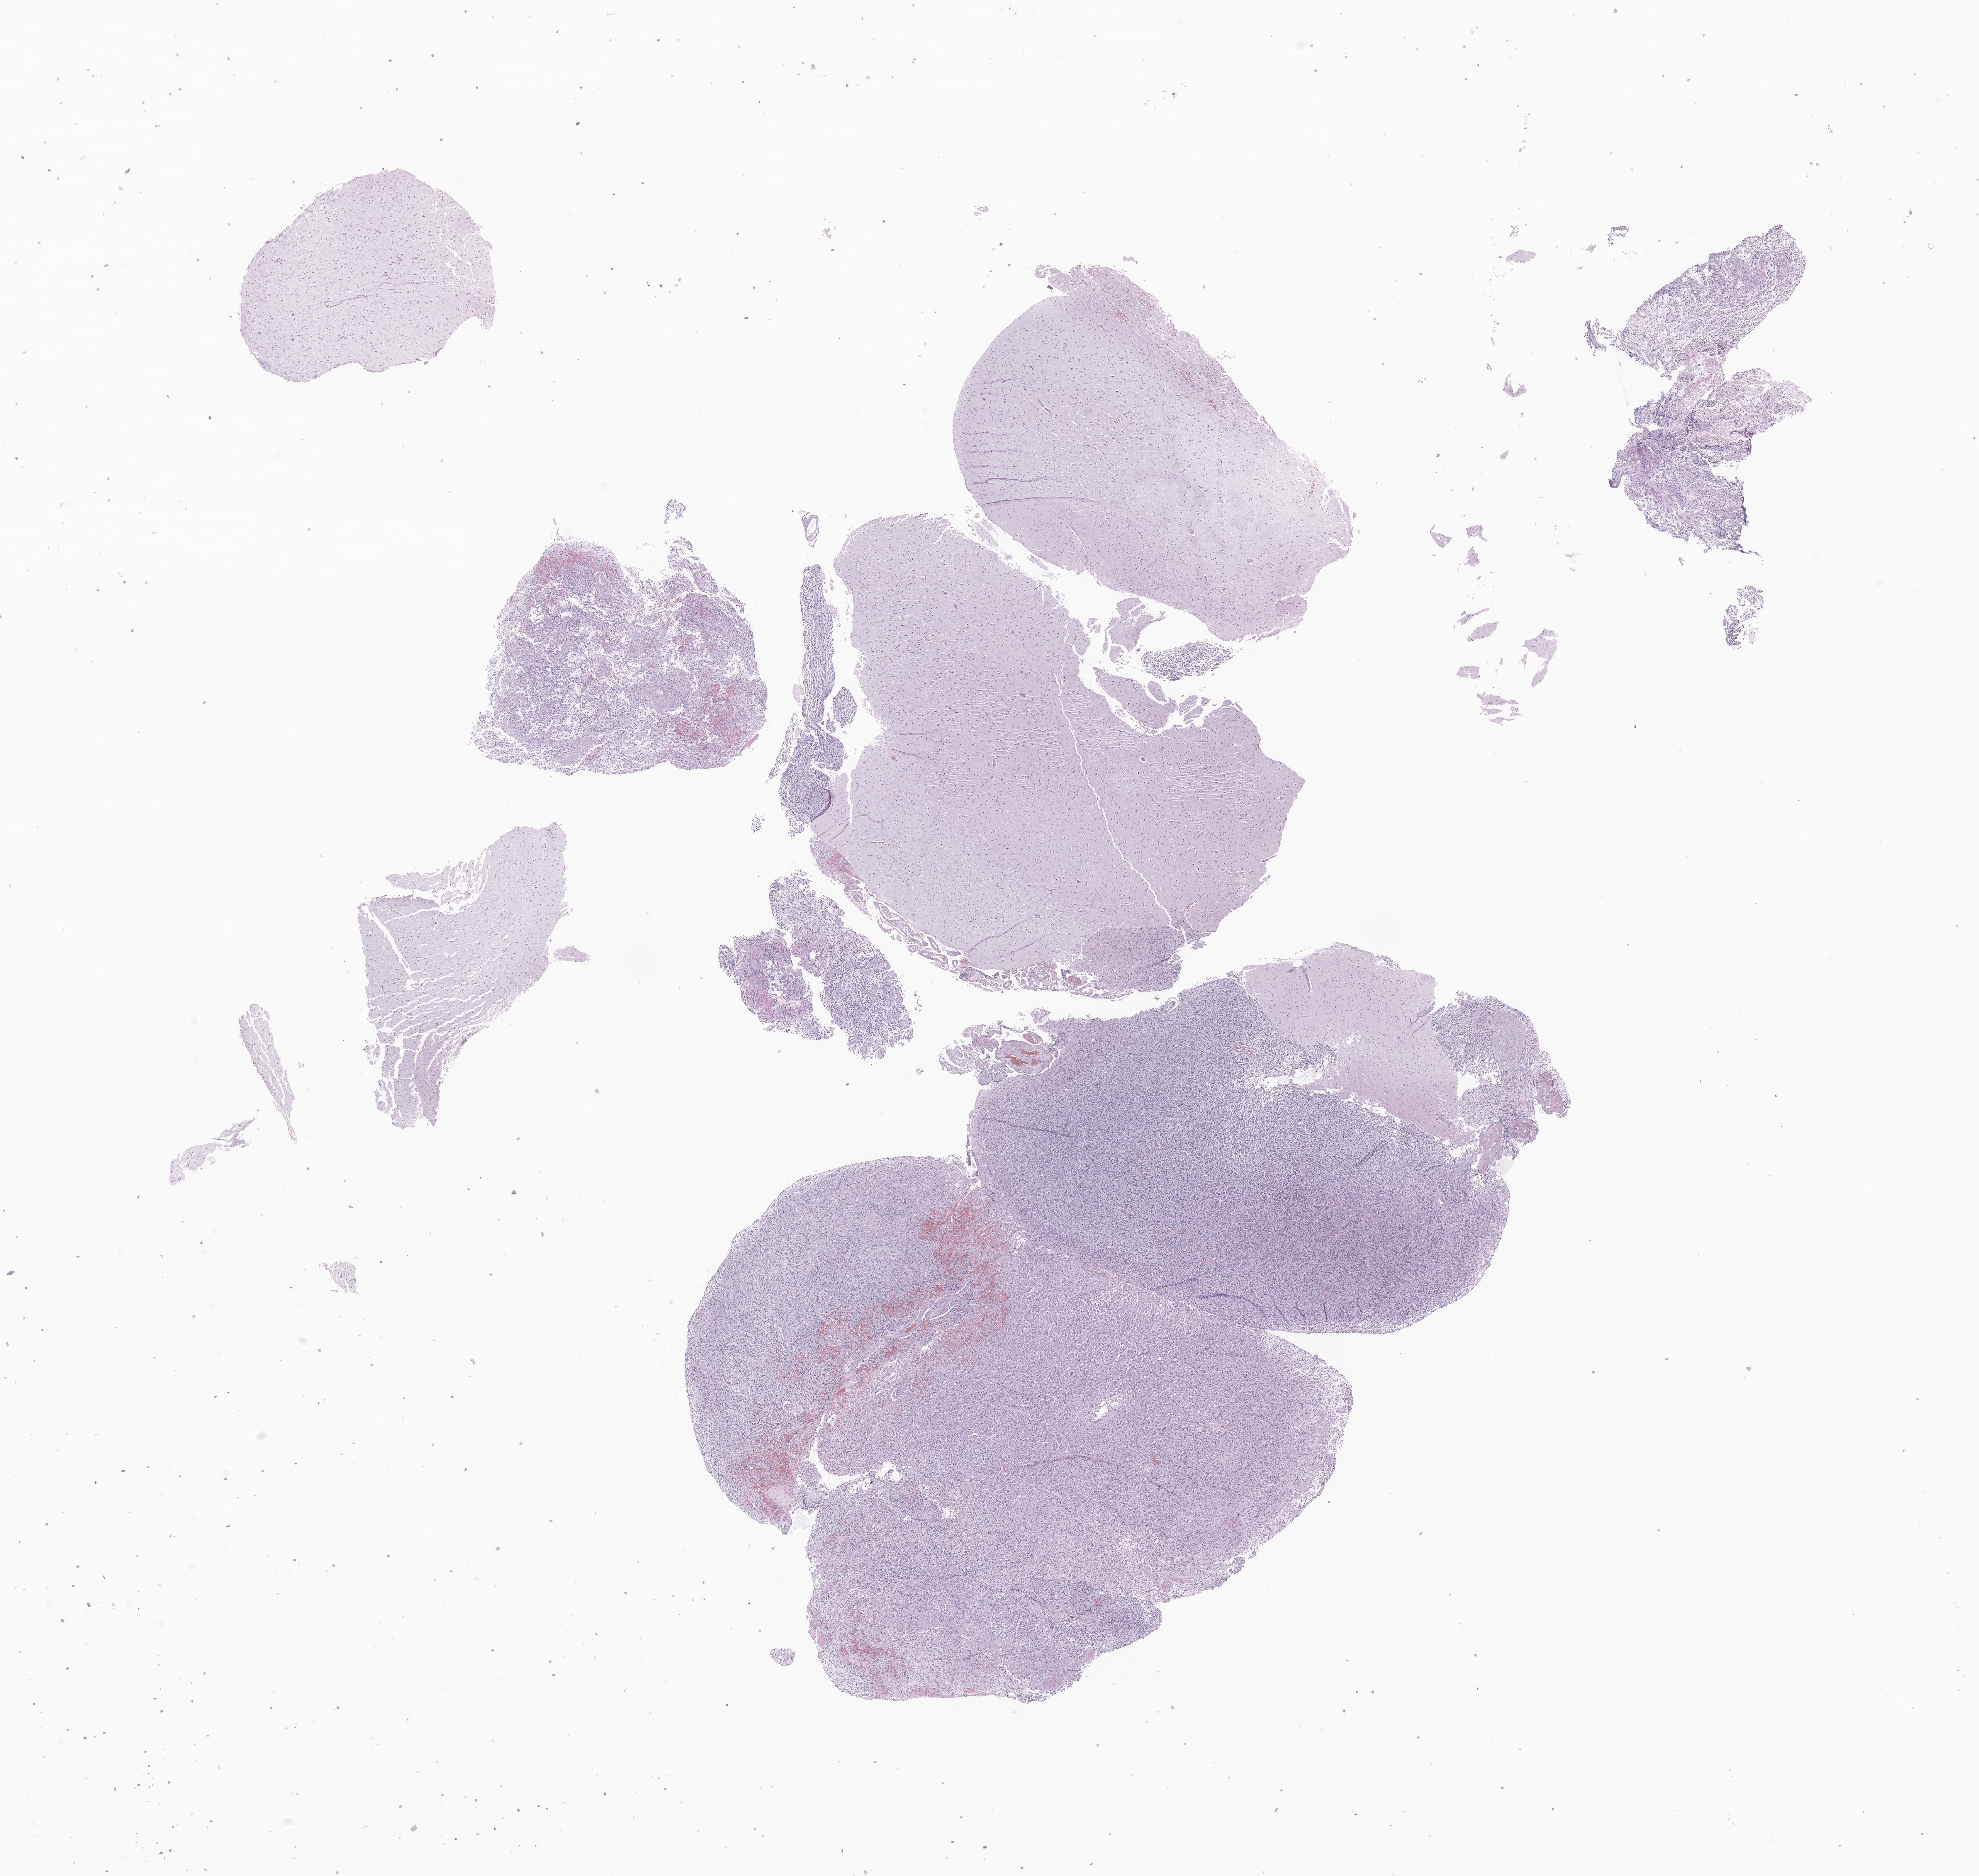
Haematoxylin and eosin whole-slide image of tumor tissue from the temporal lobe, low-resolution overview of the scanned area, about 21.6 x 20.5 mm, FFPE section. Male patient, age 304 months (25 years 4 months).
Recorded diagnosis: Glioblastoma, NOS.